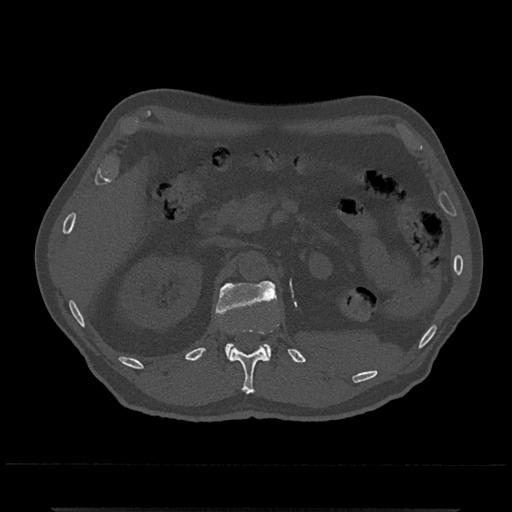
CT including the spine, one axial slice. Bone window (W 1800 / L 400 HU). 0.5 mm slice thickness. 512 × 512 image matrix, field of view 393 × 393 mm. Patient: male, 67 years. Case-level facts recorded for this patient, not image findings: primary cancer: prostate.
Structures marked on this image (semi-automatic segmentation, software-assisted and operator-edited):
- L1 vertebra: bounding box <216,281,277,360> (left, top, right, bottom; pixels)
- T12 vertebra: <230,328,269,394>